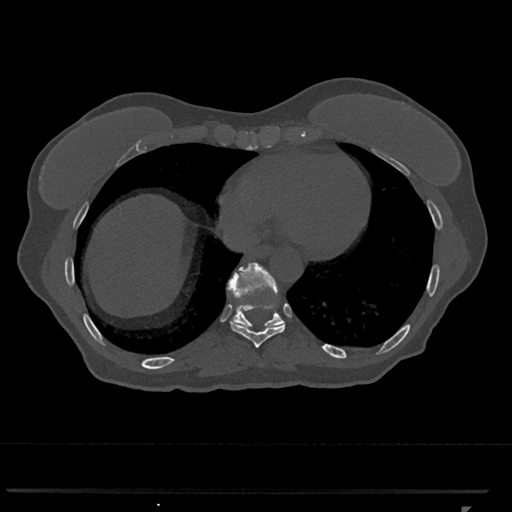
CT including the spine, one axial slice; position 603 of 793 along the scan axis; reconstruction kernel Br40s/3; 120 kVp; bone window (W 1800 / L 400 HU); 512 × 512 image matrix. Female patient, age 62 years. Case-level facts recorded for this patient, not image findings: primary cancer: renal.
Outlined on this slice (semi-automatically segmented with operator editing):
- T10 vertebra: bounding box [x1, y1, x2, y2] px = [227, 263, 284, 327]
- T9 vertebra: [230, 306, 286, 348]